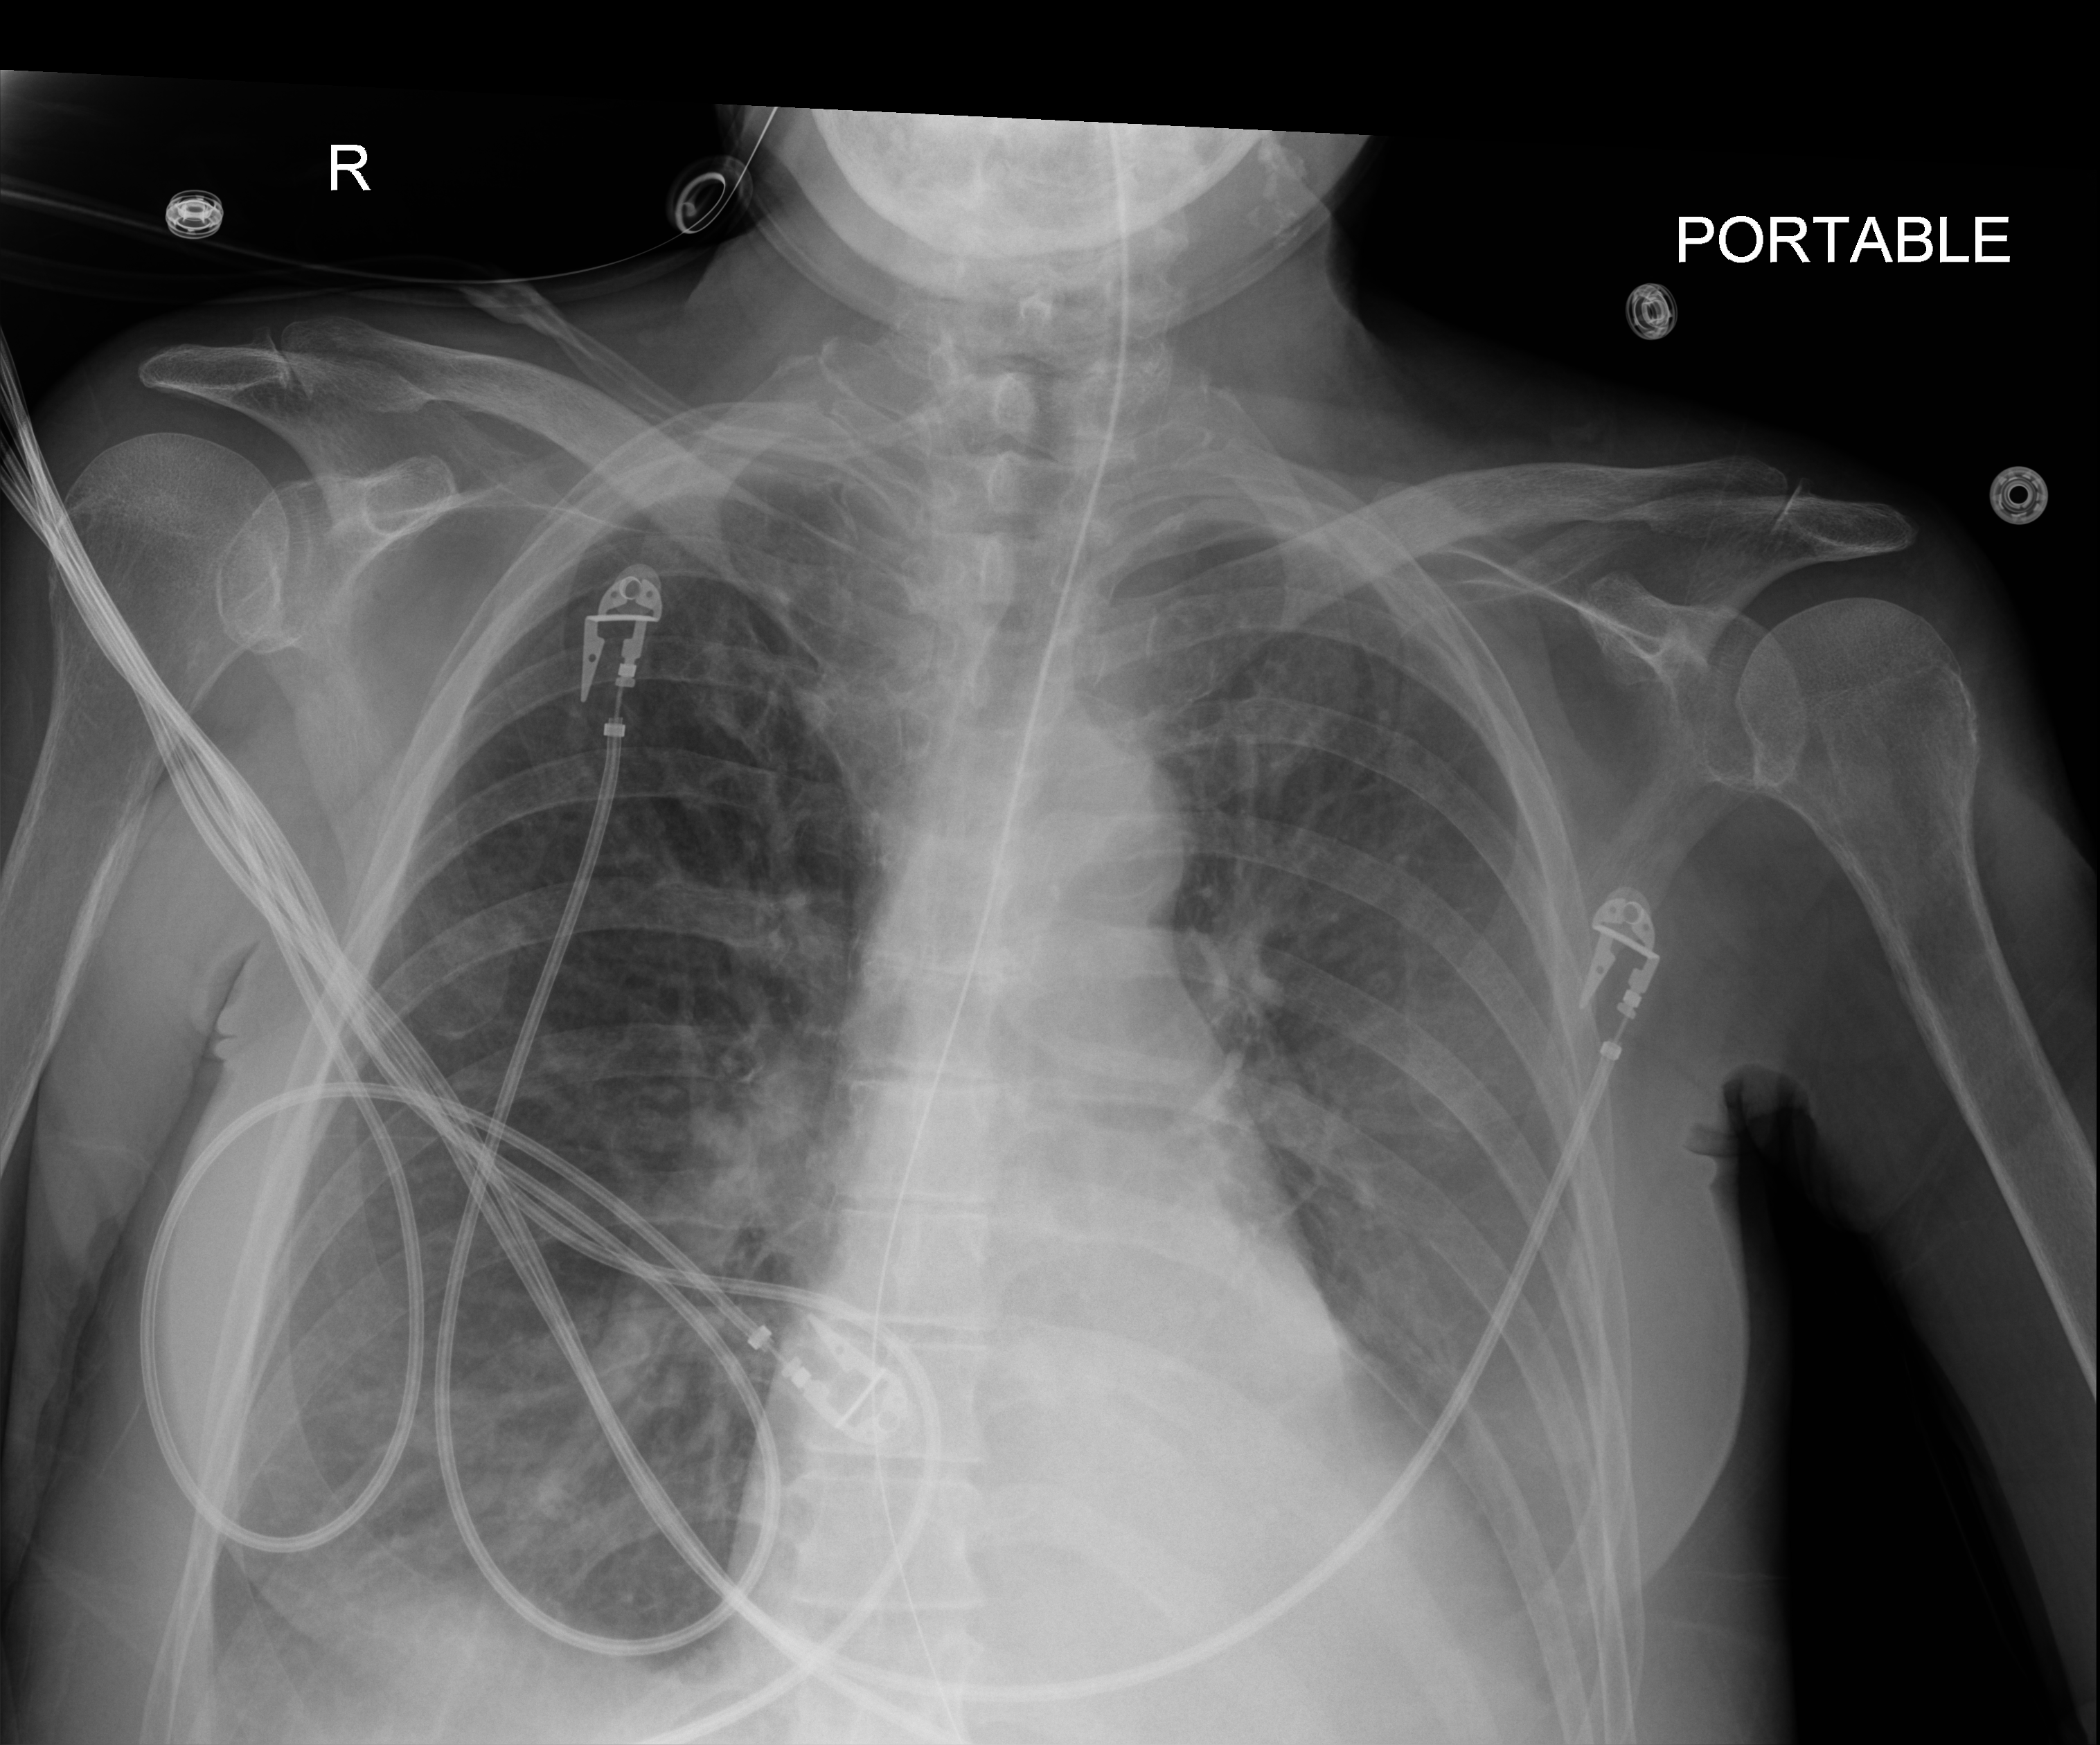
Bedside chest radiograph (digital radiography). Patient hospitalised with COVID-19; female, aged 60–74 years.
Hospital-stay facts (about this admission, not read from this image; timing relative to this image not recorded):
- mechanically ventilated during this hospital stay: yes
- admitted to intensive care during this hospital stay: yes